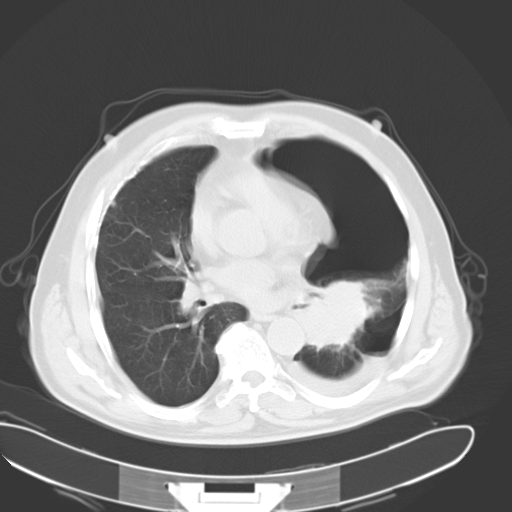
Chest CT, one axial slice. Position 18 of 34 along the scan axis. Reconstruction kernel B40f. Lung window (W 1500 / L -600 HU). 10 mm slice thickness. 512 × 512 image matrix. Male patient, age 62 years. Case-level facts recorded for this patient, not image findings: clinical TNM (as recorded): T3 N0 M1.
Structures marked on this image (rectangle marked by the reading radiologist):
- lung tumour (recorded histology: adenocarcinoma): bounding box (x1, y1, x2, y2) in pixels: (293, 279, 376, 353)
- lung tumour (recorded histology: adenocarcinoma): (306, 280, 371, 348)